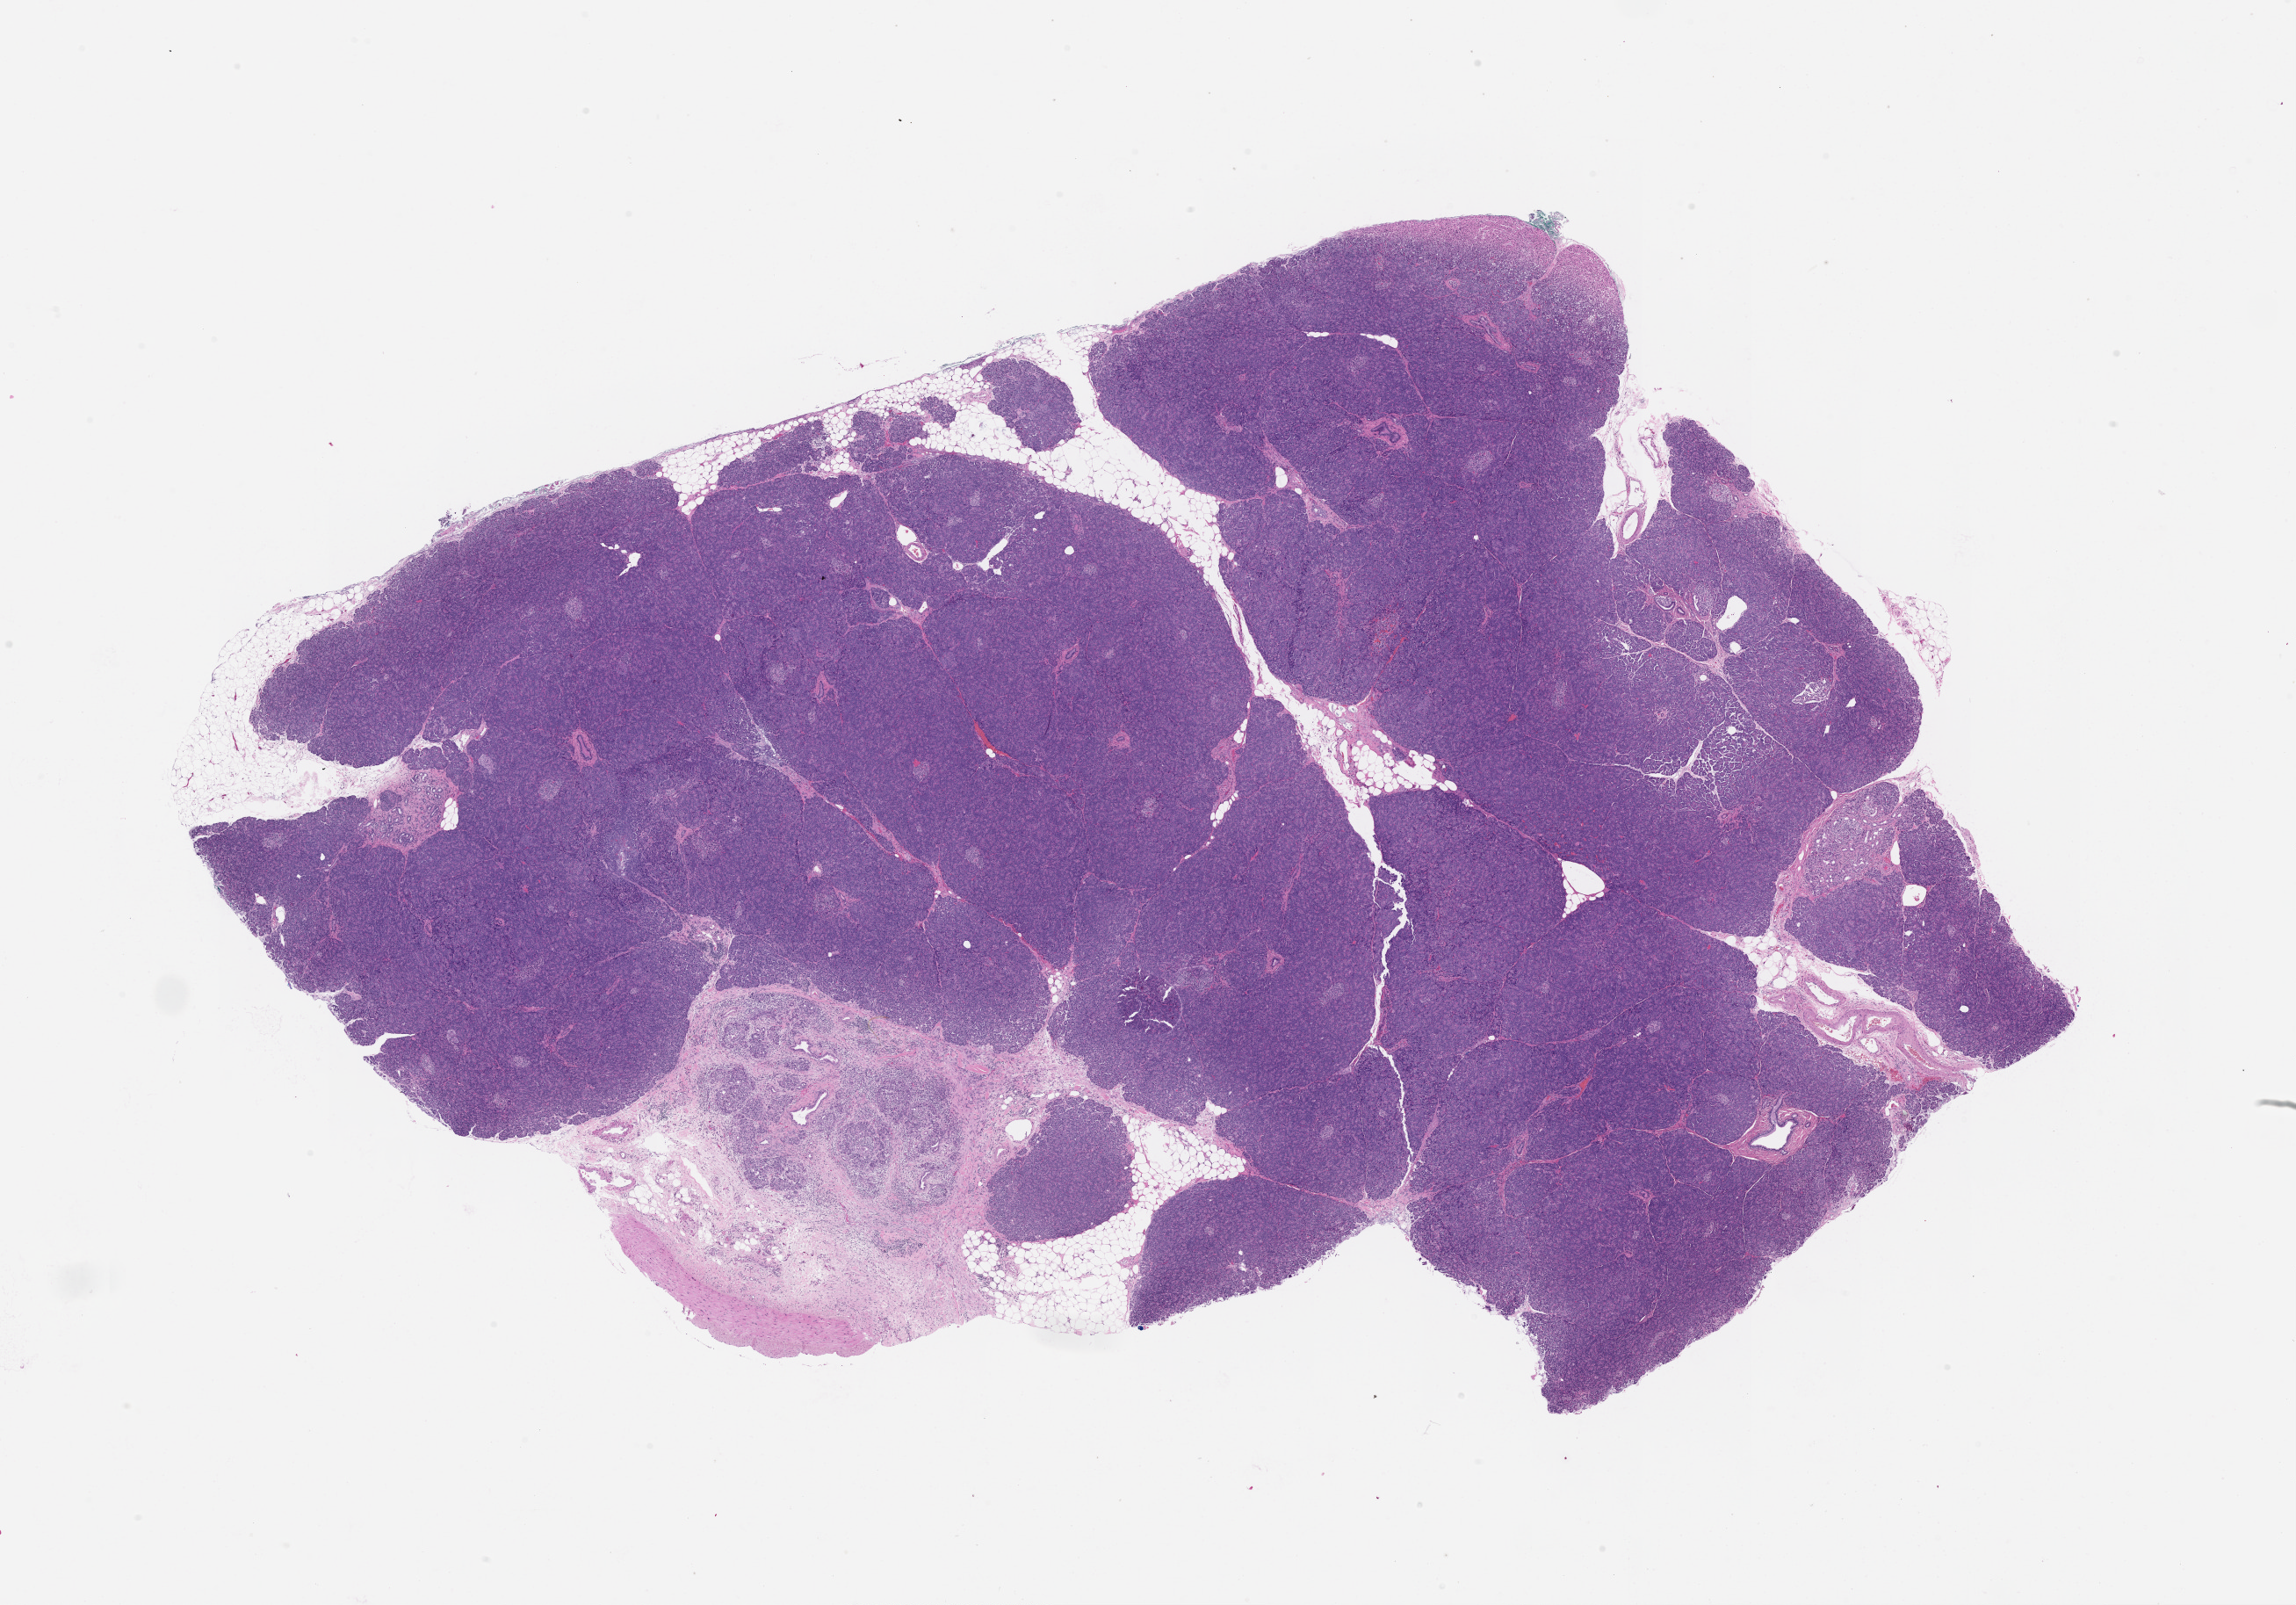
Digitized Hematoxylin and eosin (H&E) stained tissue section (whole slide) — a low-resolution overview of the entire scanned area, about 21.0 x 14.7 mm (slide scanned at 20x); pancreas, normal (non-tumour) tissue. 53-year-old male patient.
This section: normal (non-tumour) tissue from the same patient. Patient diagnosis (cohort enrolment): ductal adenocarcinoma (pancreas).